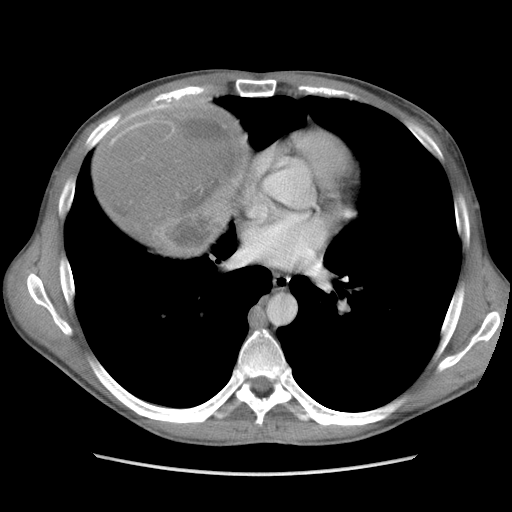
Contrast-enhanced abdominal CT, one axial slice. Position 102 of 115 along the scan axis. Soft-tissue window (W 400 / L 40 HU). 5 mm slice thickness. 512 × 512 image matrix. Male patient. From the clinical record (not read from this slice): diagnosis: adrenocortical carcinoma; tumour side: right adrenal; Ki-67 index: 13 %; stage (as recorded): 3.
Outlined on this slice (semi-automatic segmentation, software-assisted and operator-edited):
- mass: bounding box [x1, y1, x2, y2] px = [99, 106, 247, 252]